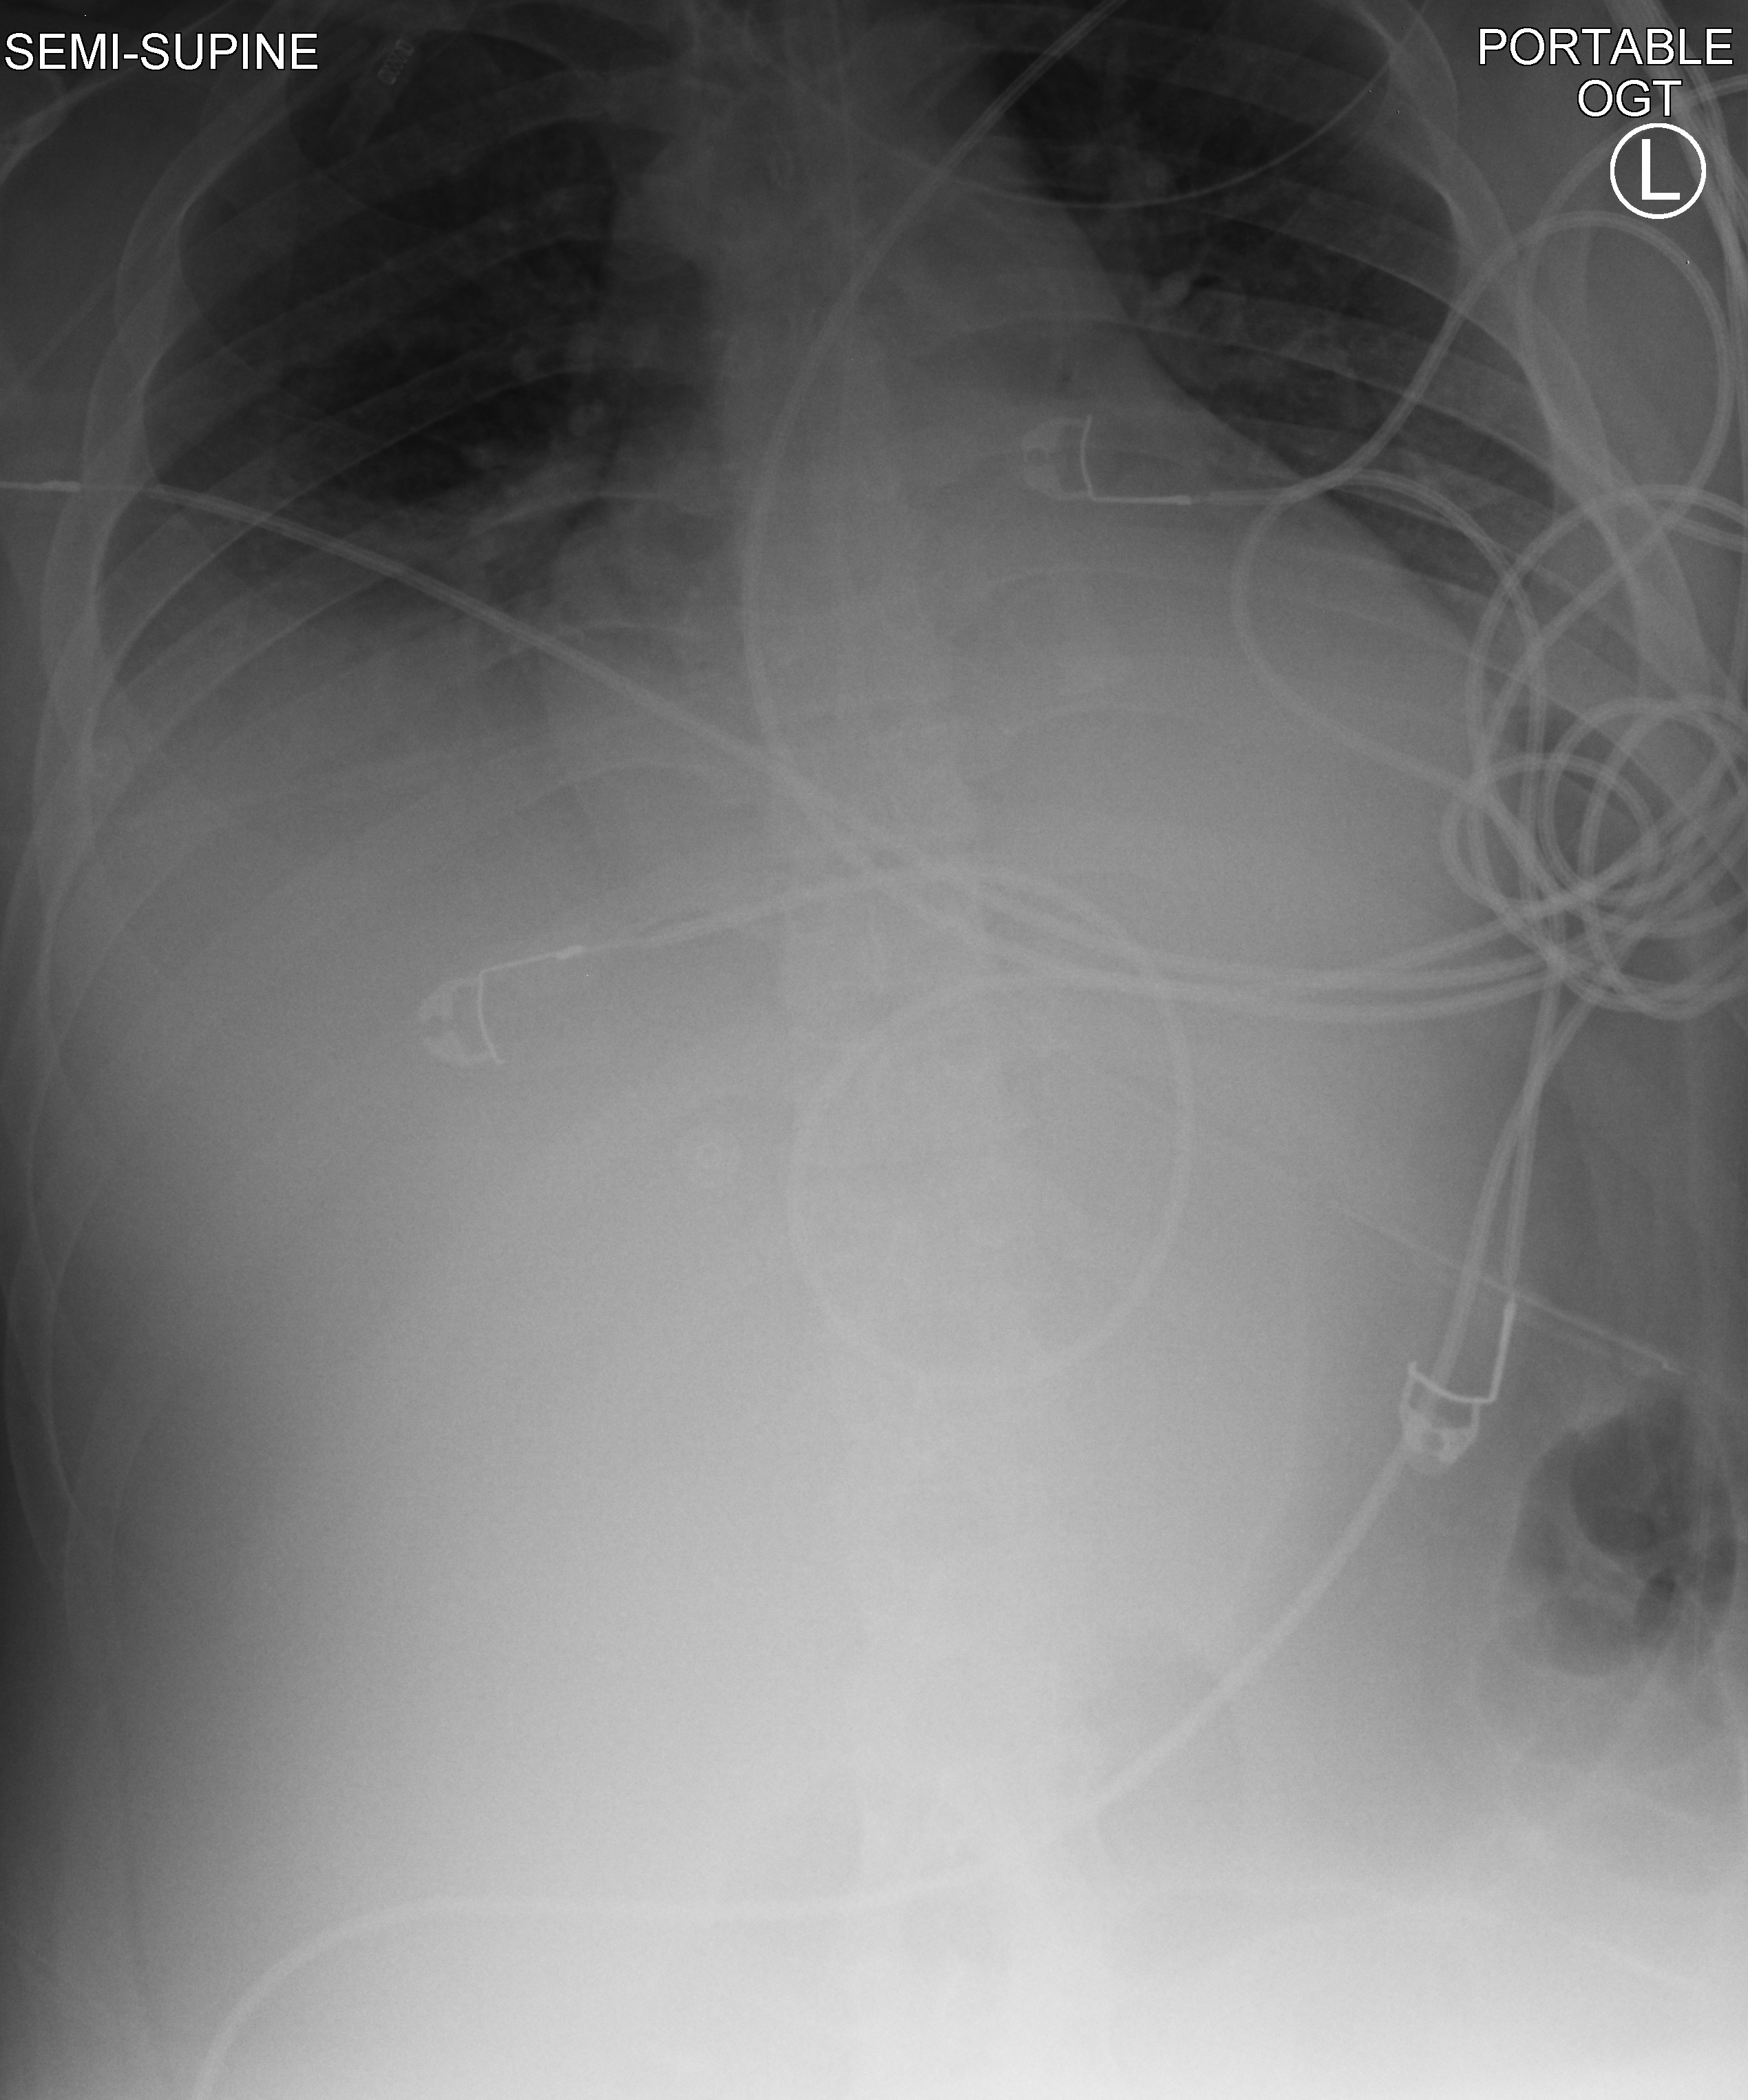
Portable chest radiograph. Patient hospitalised with COVID-19; male, aged 18–59 years.
From the hospital-stay record, not from the radiograph (when in the stay this image was taken is not recorded): mechanically ventilated during this hospital stay: yes.